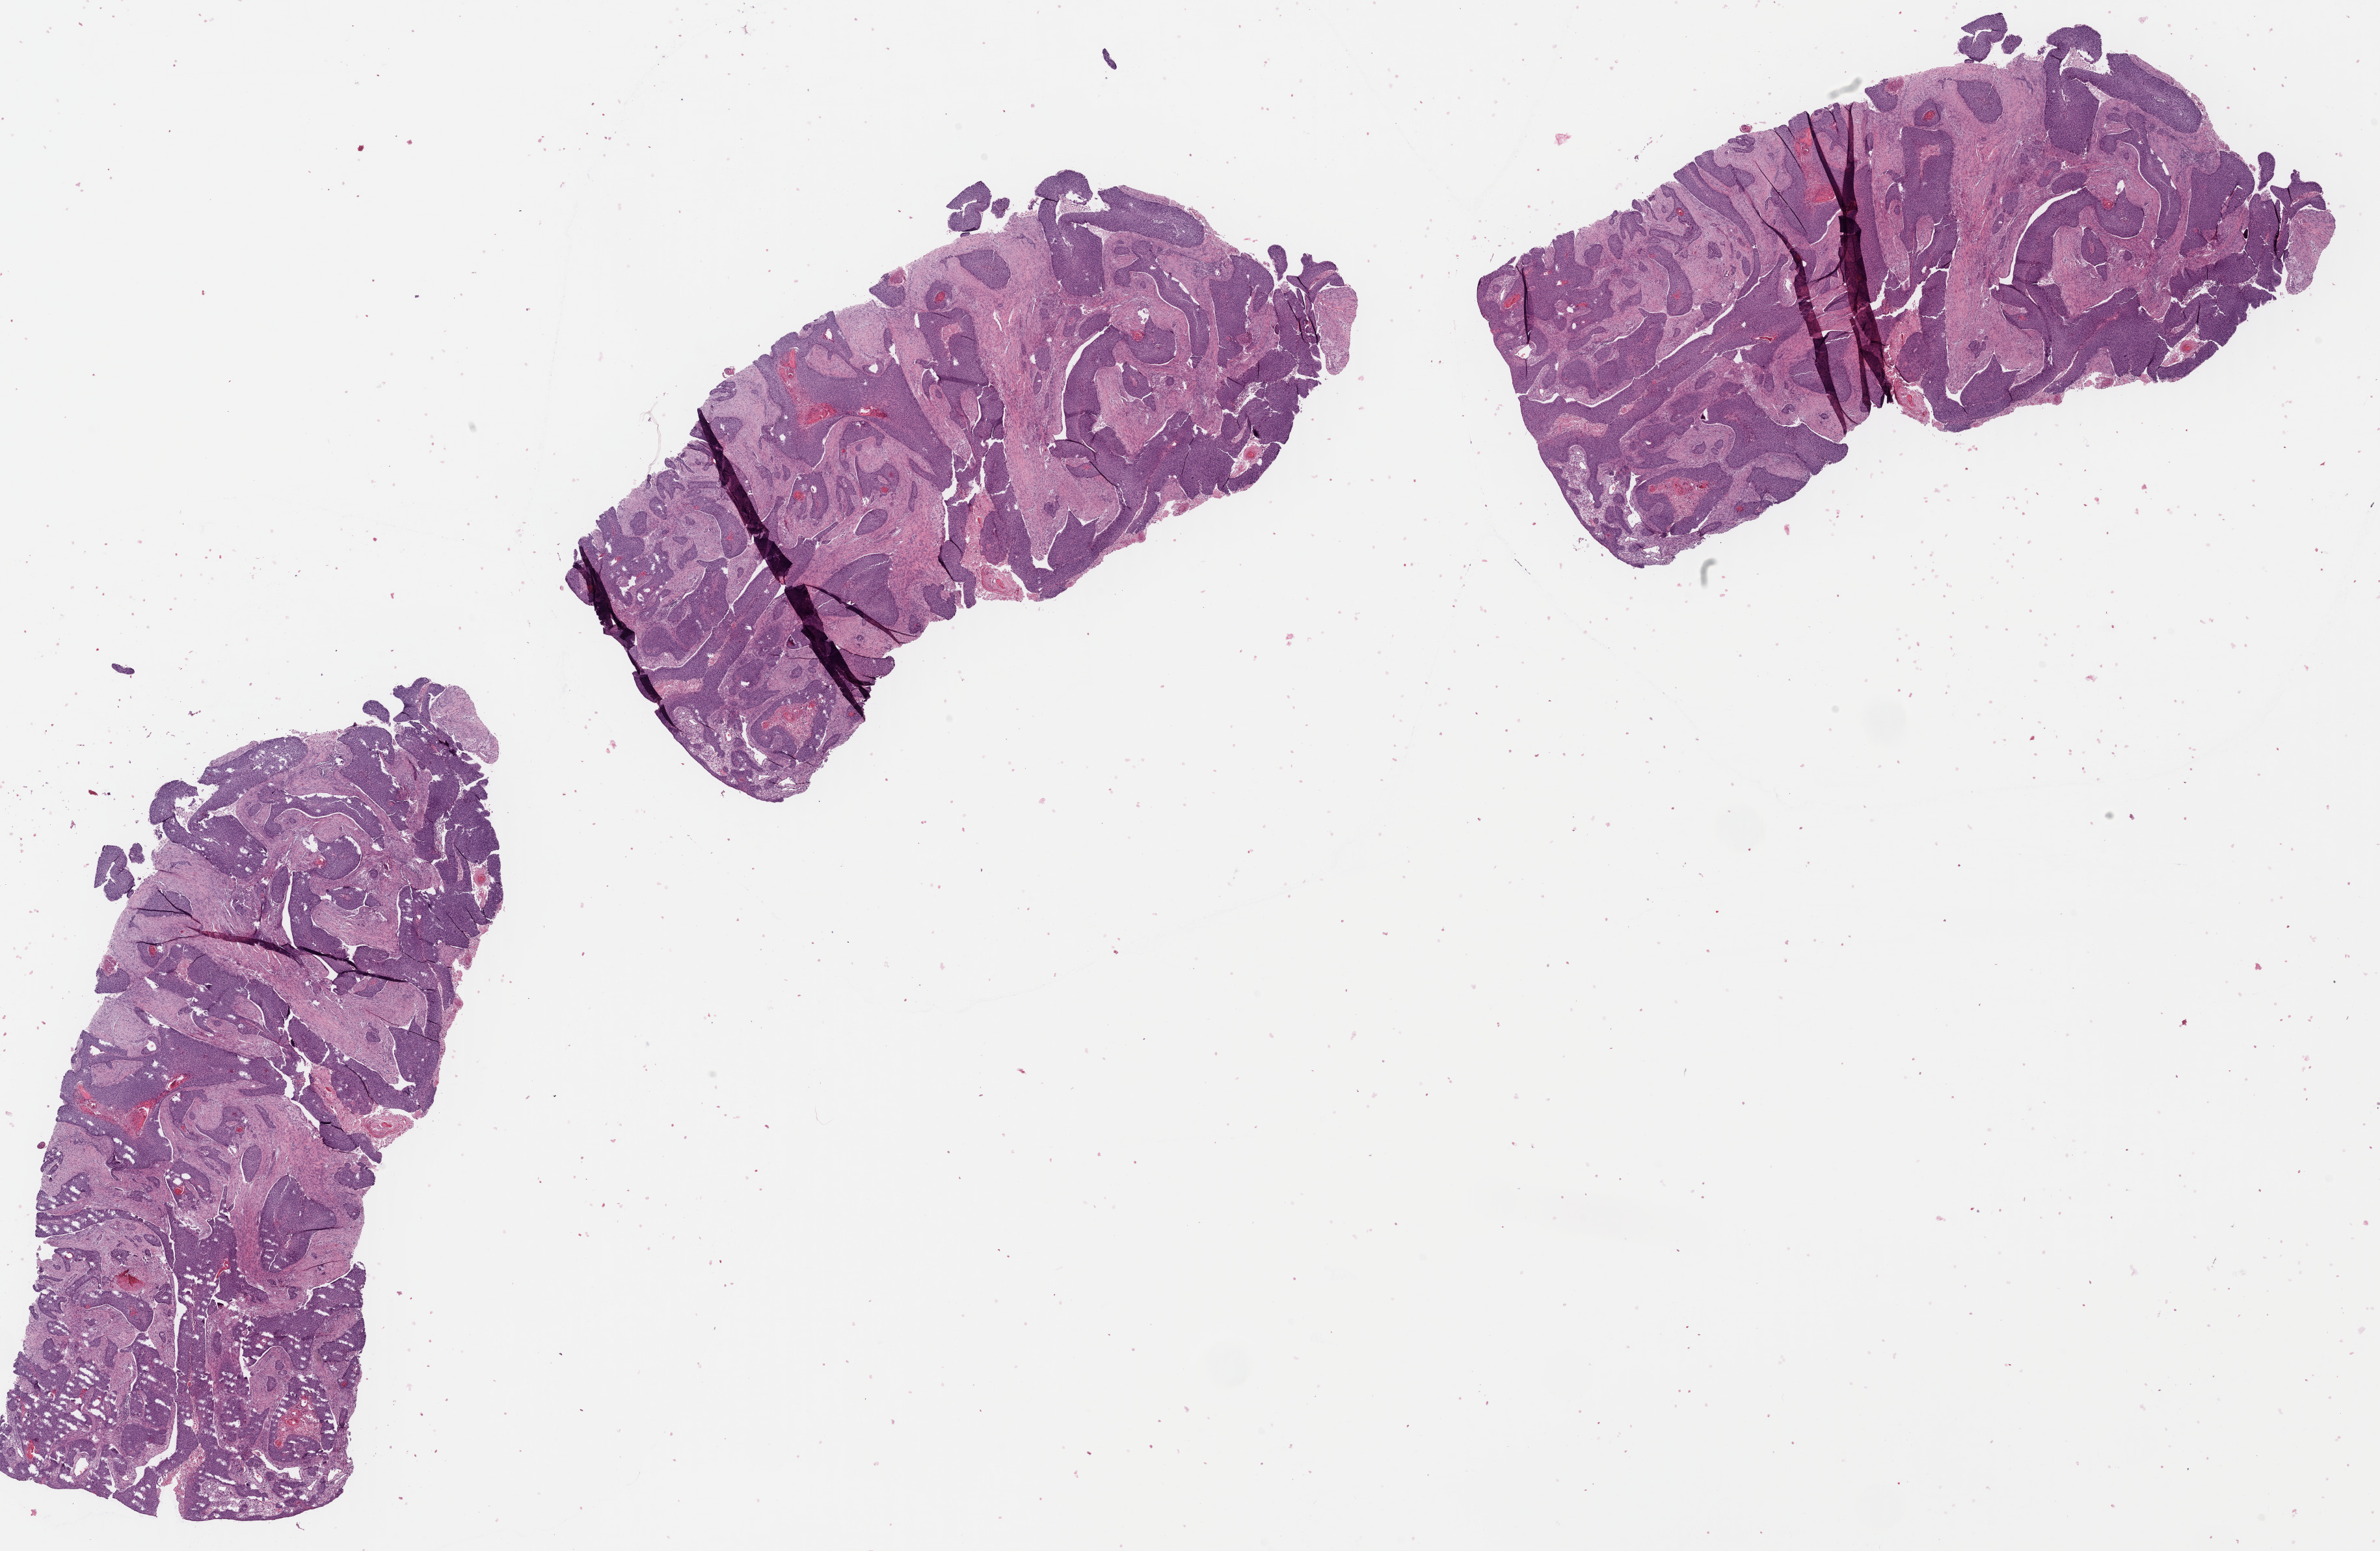
Digitized H&E tissue section (whole slide), shown as a low-resolution overview of the whole scanned area (about 28.8 x 18.7 mm, slide scanned at 40x). Formalin-fixed paraffin-embedded (FFPE) diagnostic section. Primary tumour sample from the esophagus. Patient: male, age at initial diagnosis 51 years. Histologic grade: G1 (well differentiated).
Pathologic diagnosis: Squamous cell carcinoma, NOS. TNM: T2 N0 MX. AJCC pathologic stage: IB (7th edition).